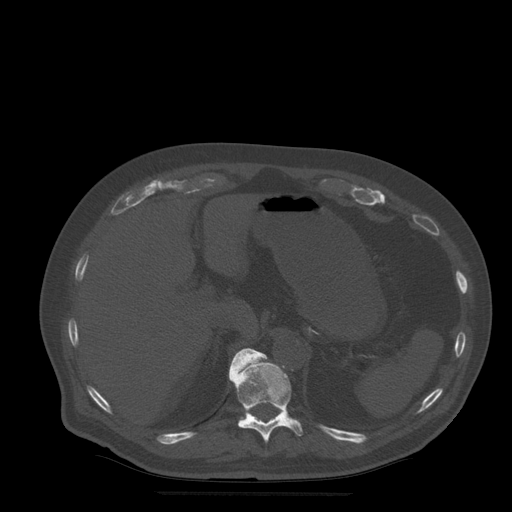
CT including the spine, one axial slice; position 242 of 522 along the scan axis; bone window (W 1800 / L 400 HU); 1.25 mm slice thickness; 512 × 512 image matrix. Patient age 72 years. Case-level facts recorded for this patient, not image findings: primary cancer: prostate.
Annotated regions visible in this slice (semi-automatic segmentation, software-assisted and operator-edited):
- T11 vertebra: bounding box <229,348,303,443> (left, top, right, bottom; pixels)
- T12 vertebra: <230,350,249,369>